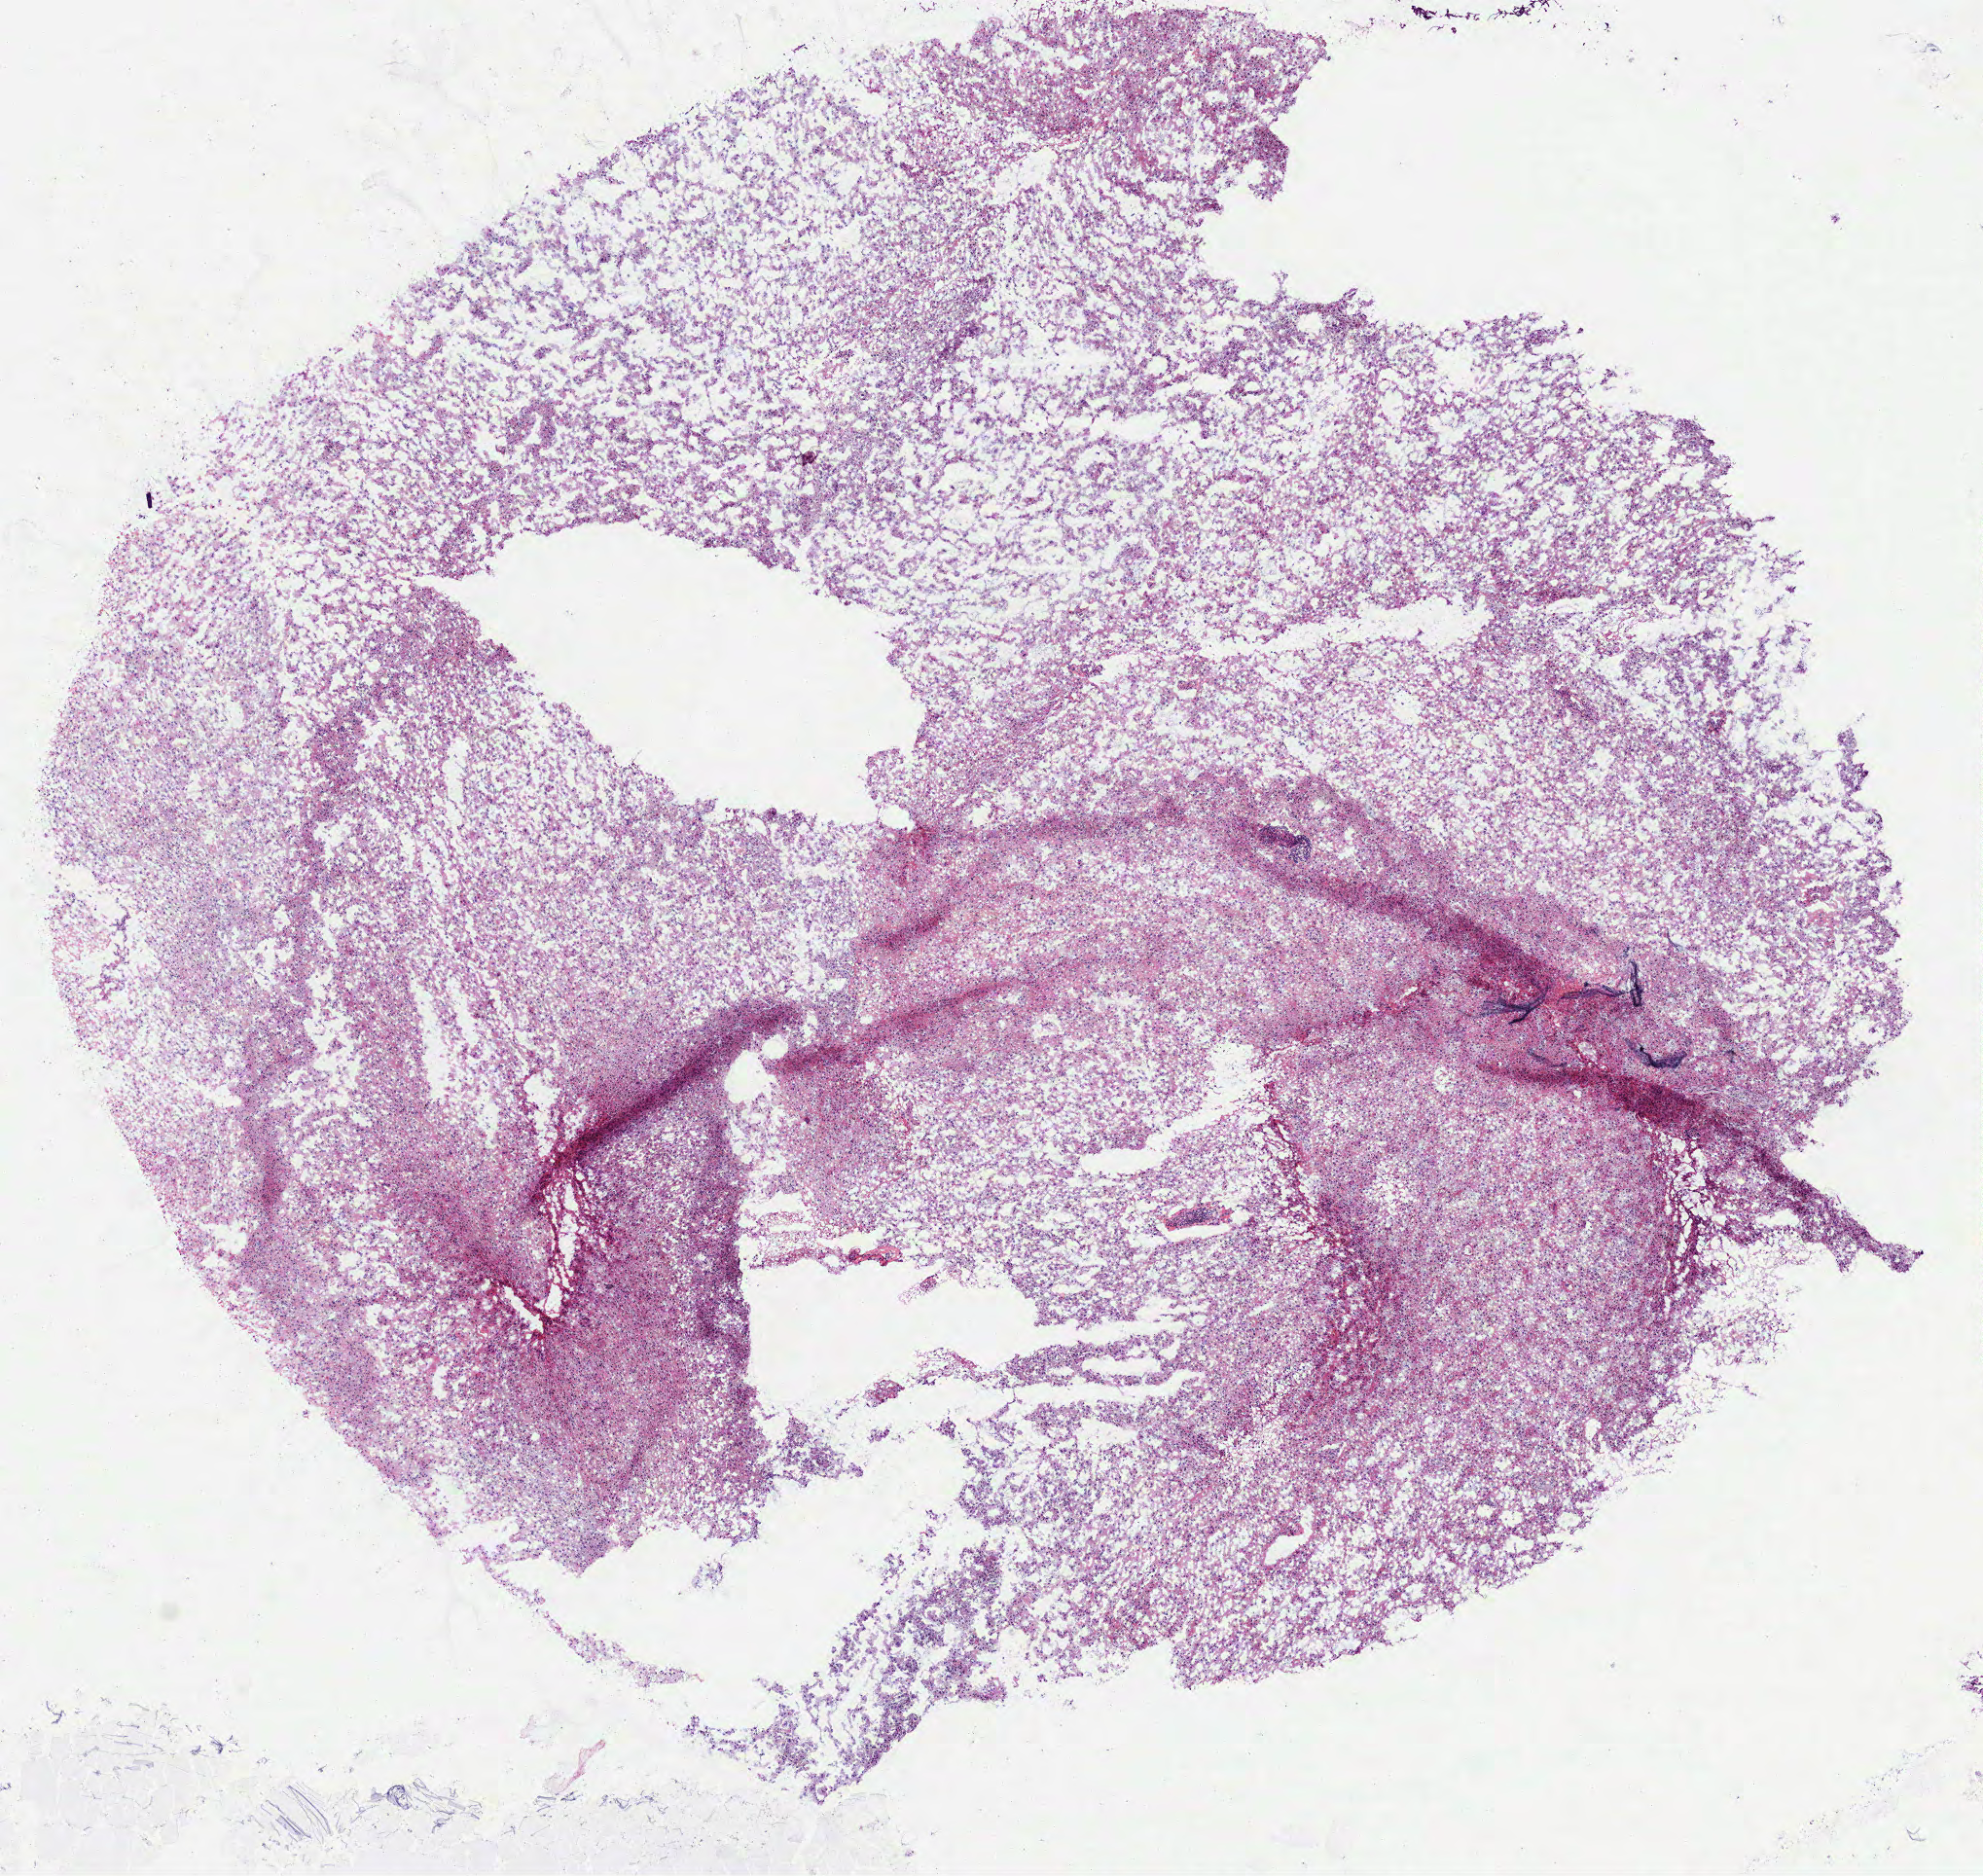
Whole-slide histology image, H&E, low-resolution overview of the scanned area, about 8.2 x 7.8 mm (from a 40x scan). Frozen section from the bottom of the tissue portion. Primary tumour sample from the brain. Male patient; age at initial diagnosis 28 years. Histologic grade: G2 (moderately differentiated). Slide review estimates, as recorded: tumour cells 100%, tumour nuclei 70%, normal cells 0%, stromal cells 0%, necrosis 0%.
Histologic diagnosis: Mixed glioma.